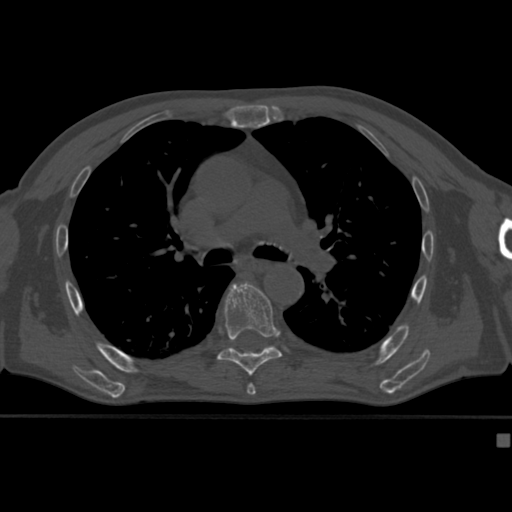
CT including the spine, one axial slice; slice 280 of 430 in the series (ordered by position); bone window (W 1800 / L 400 HU); 1.5 mm slice thickness; 512 × 512 image matrix, field of view 337 × 337 mm. Patient: male, 64 years. Case-level facts recorded for this patient, not image findings: primary cancer: uterus.
Outlined on this slice (semi-automatic segmentation, software-assisted and operator-edited):
- T7 vertebra: bounding box <217,282,287,376> (left, top, right, bottom; pixels)